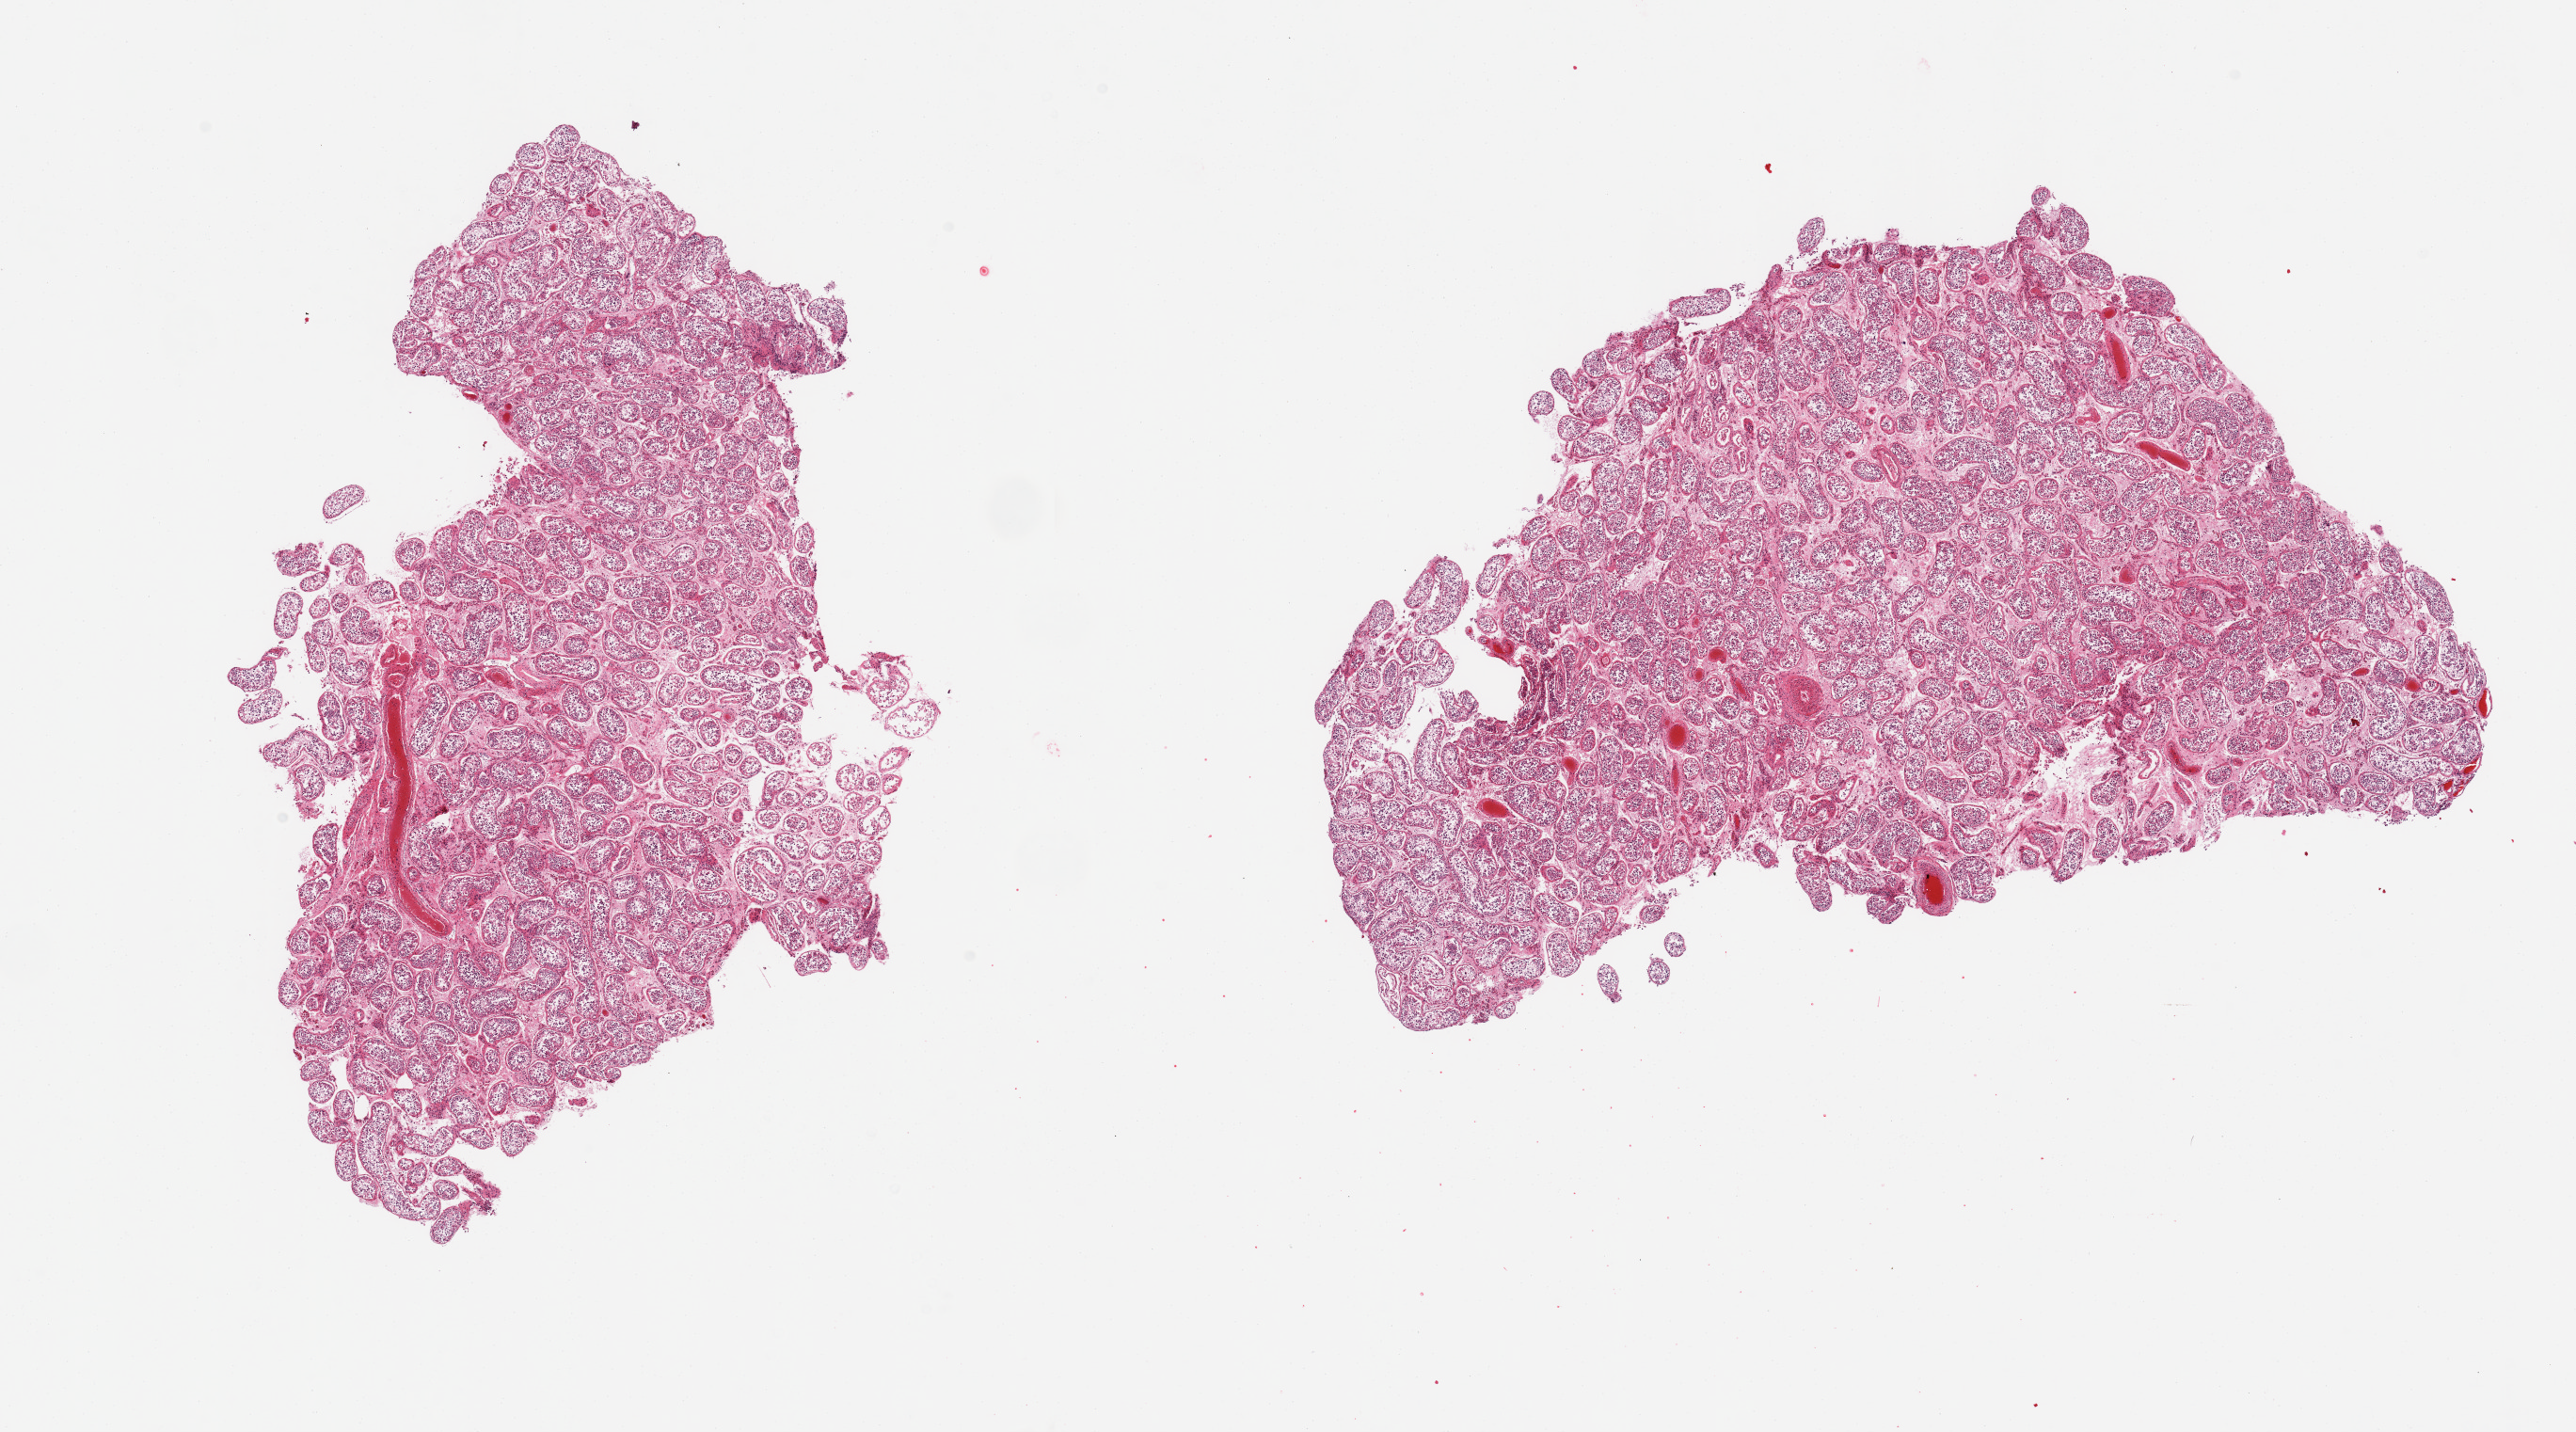
Whole-slide image, hematoxylin and eosin (H&E) stain, brightfield — low-resolution overview of the scanned area, about 21.7 x 12.0 mm (slide scanned at 20x); PAXgene-fixed, paraffin-embedded tissue; sampled site (target tissue): testis; tissue donor sample.
* pathologist's review note for this sample: 2 pieces, moderately advanced autolysis